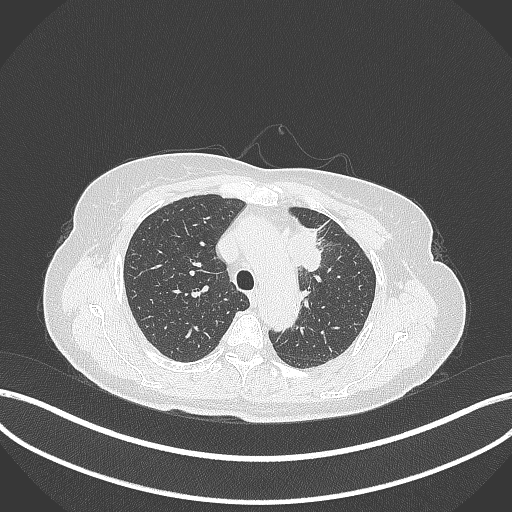
Chest CT, one axial slice. Slice 247 of 369 in the series (ordered by position). Reconstruction kernel B70f. 120 kVp. Lung window (W 1500 / L -600 HU). 1 mm slice thickness. 512 × 512 image matrix, field of view 400 × 400 mm. Female patient, age 65 years. Case-level facts recorded for this patient, not image findings: clinical TNM (as recorded): T2a N0 M0; histopathological grade: G2-3.
Outlined on this slice (rectangle marked by the reading radiologist):
- lung tumour (recorded histology: adenocarcinoma): bounding box (x1, y1, x2, y2) in pixels: (285, 227, 325, 273)